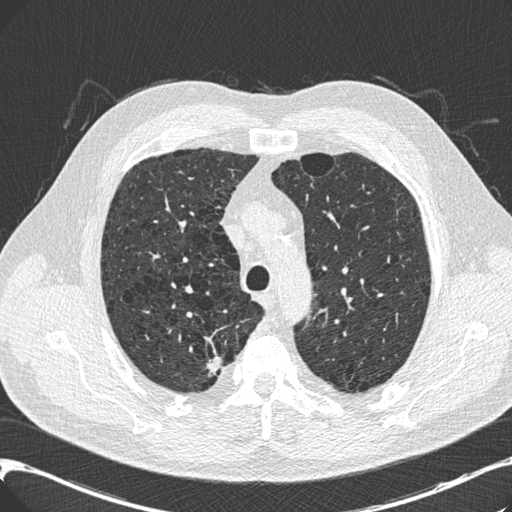
Low-dose screening chest CT, one axial slice; position 150 of 197 along the scan axis; lung window (W 1500 / L -600 HU); 0.75 mm slice thickness; 512 × 512 image matrix, field of view 367 × 367 mm.
Annotated regions visible in this slice (expert manual segmentation):
- lesion 1 (tumor, upper lobe of right lung): bounding box [x1, y1, x2, y2] px = [207, 352, 222, 374]